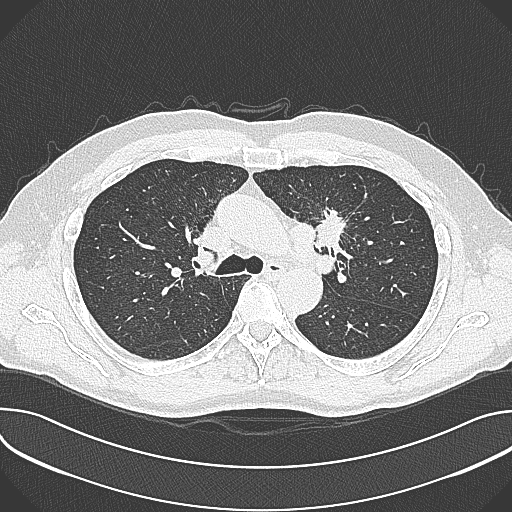
Chest CT (low-dose screening protocol), one axial image; baseline annual screen; lung window (W 1500 / L -600 HU); 1 mm slice thickness; lung (sharp) reconstruction kernel (B80f); 120 kVp; 512 × 512 image matrix, field of view 380 × 380 mm. Male participant, aged 59 years at enrolment. Current smoker at enrolment.
Lesion marked by an expert reader, box from (x=303, y=195) to (x=363, y=257) px. The screening reader recorded 2 non-calcified nodules or masses ≥4 mm on this exam (left upper lobe, left upper lobe); which of them this box marks is not recorded. Later outcome: lung cancer diagnosed 21 days after this screen — non-small cell carcinoma, left upper lobe, poorly differentiated (G3), stage IIIA (AJCC 6th edition), 35 mm at pathology.